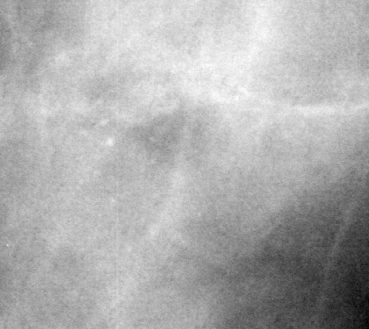
Crop from a digitized film mammogram around one marked abnormality; left breast; CC view.
- Calcifications, morphology punctate, distribution clustered; BI-RADS assessment category 4; subtlety rating 3 on a 1 (subtle) to 5 (obvious) scale; pathology (as recorded): benign.